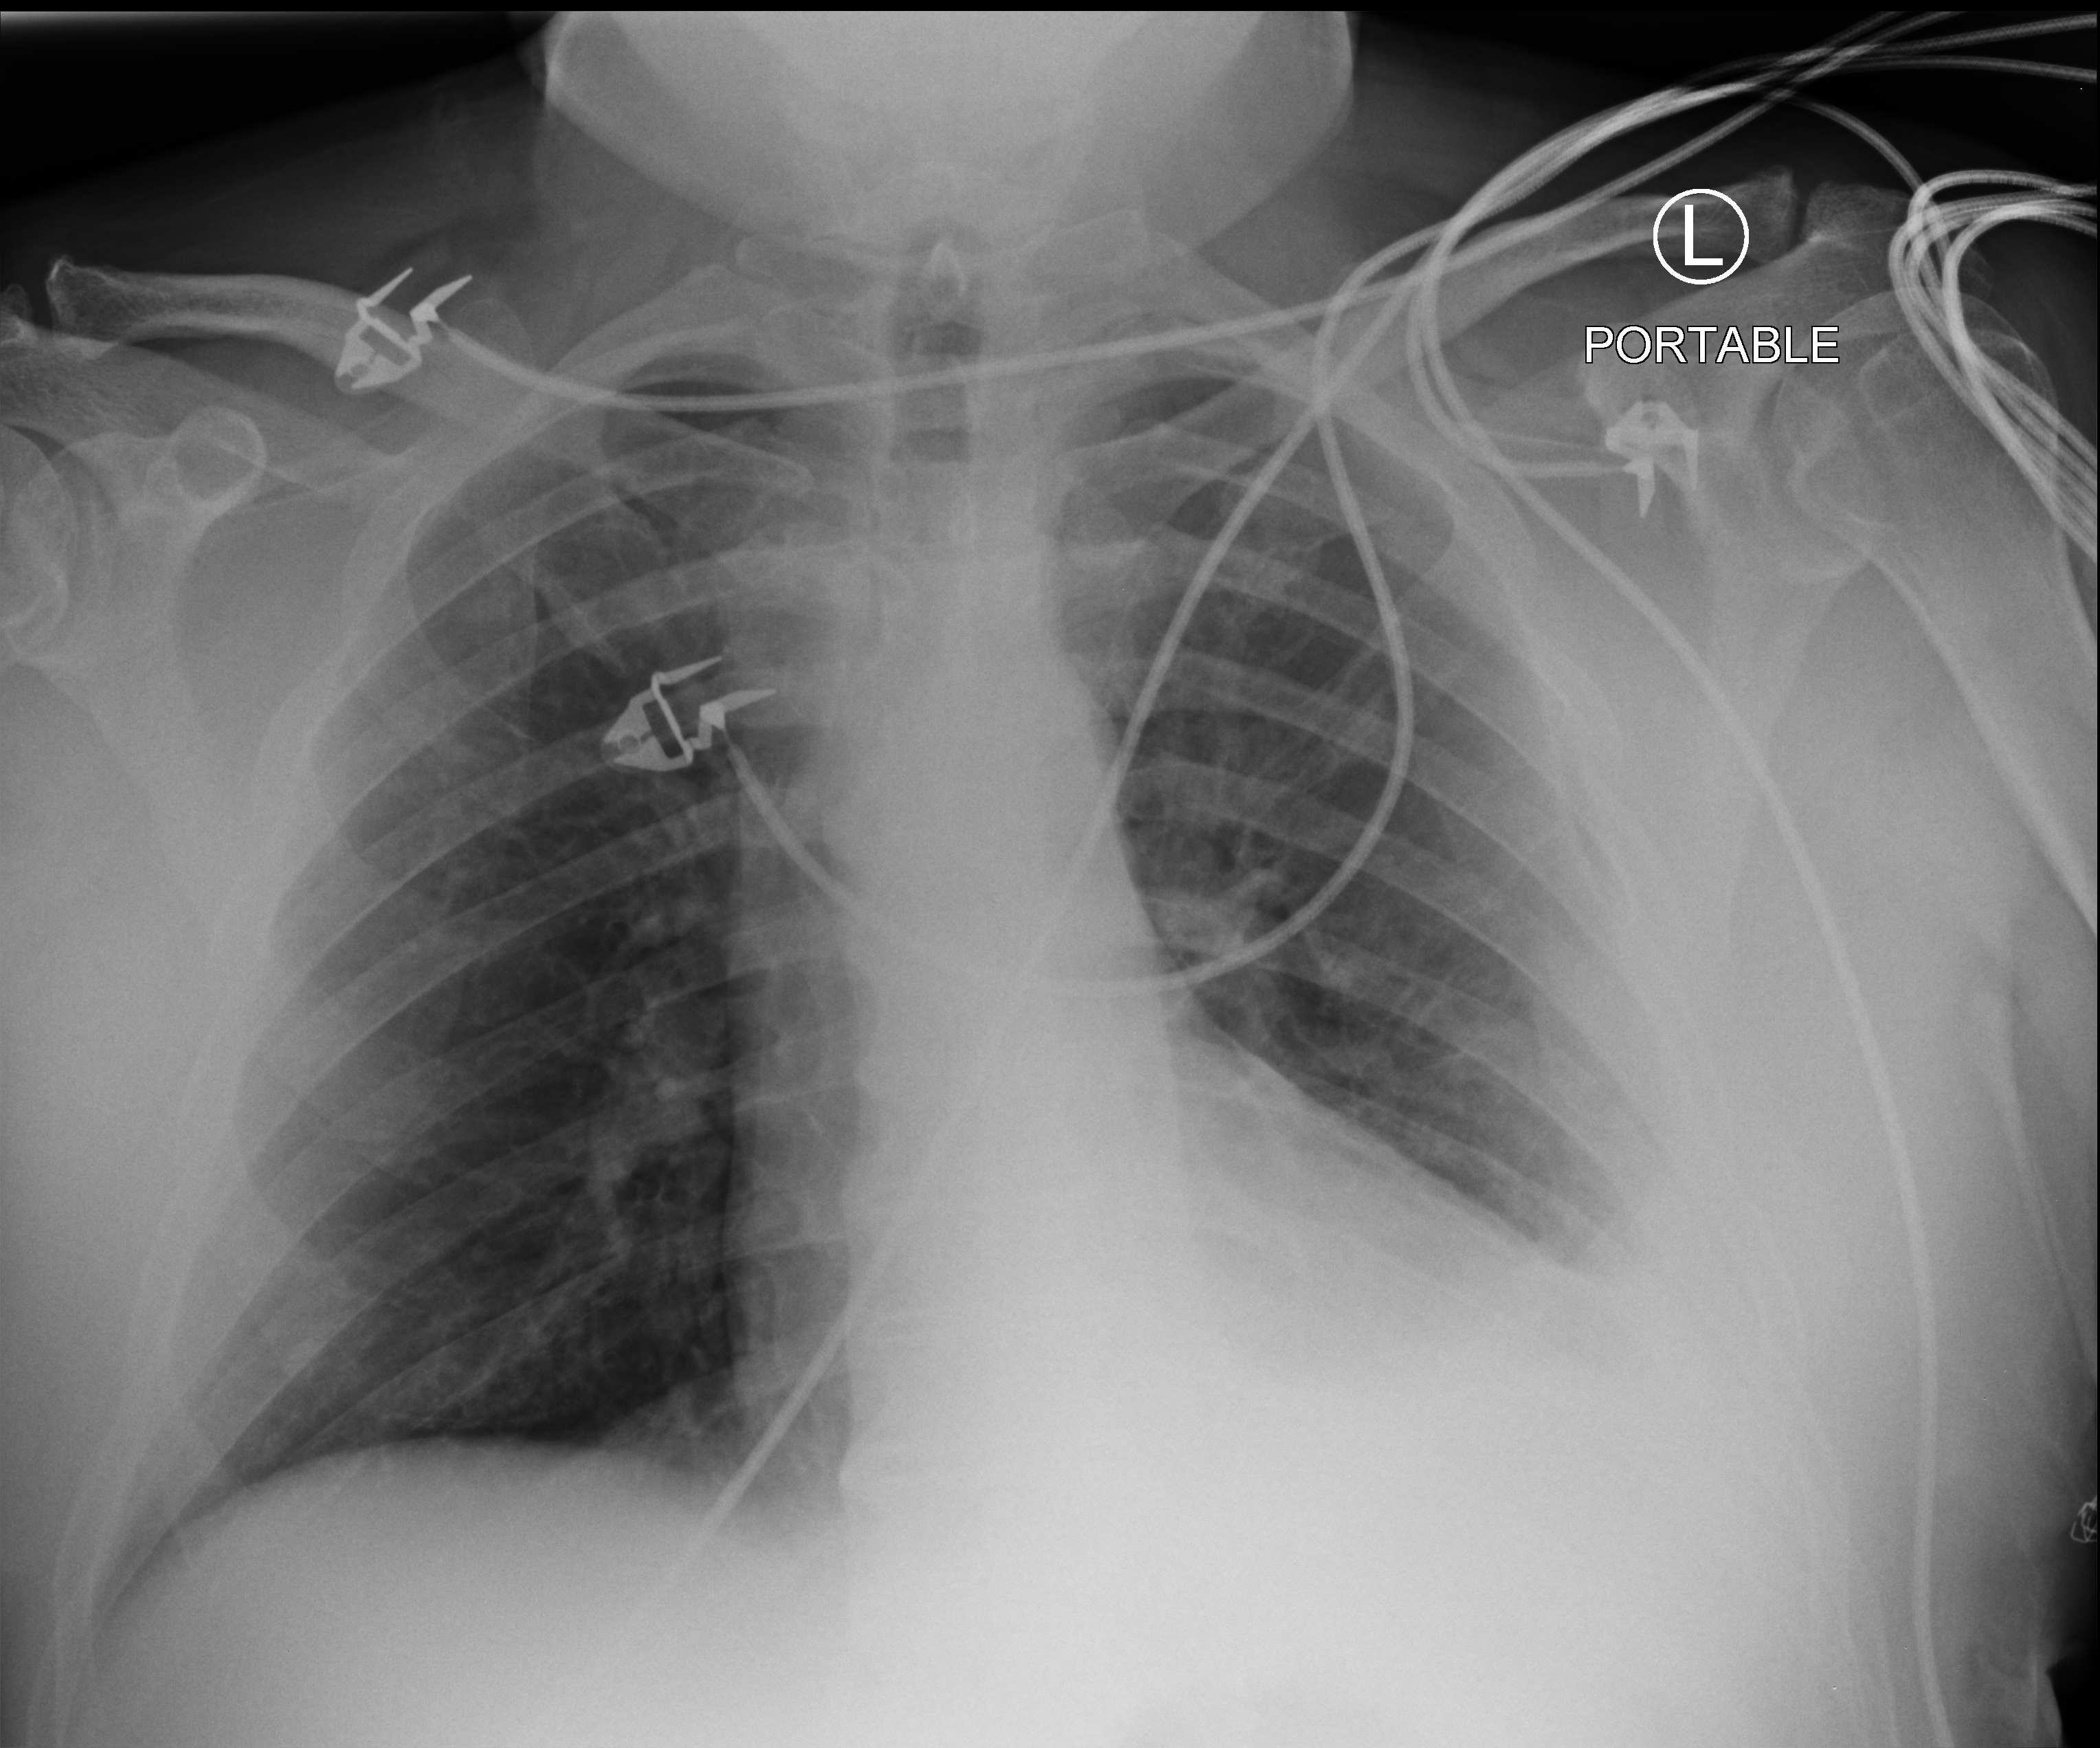
Portable chest radiograph. Patient hospitalised with COVID-19; male, aged 18–59 years.
Hospital-stay facts (about this admission, not read from this image; timing relative to this image not recorded): mechanically ventilated during this hospital stay: no.